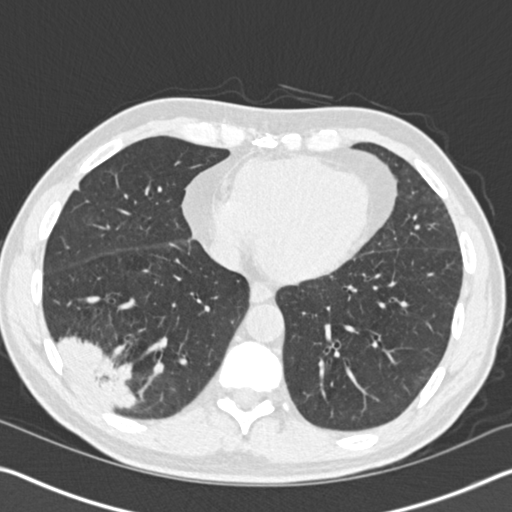
Axial slice from a low-dose chest CT screening exam, baseline screening round, lung window (W 1500 / L -600 HU), 120 kVp, slice 107 of 161 in the series, 512 × 512 image matrix. Male participant, aged 61 years at enrolment. Current smoker at enrolment.
• Expert-annotated lung lesion, bounding box [x1, y1, x2, y2] px = [32, 305, 149, 420].
• Screening reader's record for this exam (one nodule recorded; not confirmed to be the boxed lesion): non-calcified nodule or mass ≥4 mm, right lower lobe, 52 × 36 mm, spiculated (stellate) margins, soft tissue attenuation.